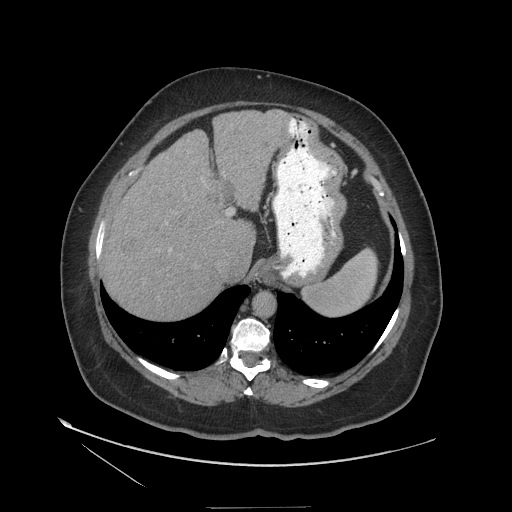
Contrast-enhanced abdominal CT (liver protocol), one axial slice; position 89 of 127 along the scan axis; reconstruction kernel STANDARD; 140 kVp; soft-tissue window (W 400 / L 40 HU); 2.5 mm slice thickness; 512 × 512 image matrix, field of view 480 × 480 mm. From the clinical record (not read from this slice): diagnosis: hepatocellular carcinoma (patient treated with transarterial chemoembolisation; whether this scan precedes or follows treatment is not stated here); TNM stage (as recorded): Stage-II; Child-Pugh class: A; tumour differentiation: well differentiated; tumour nodularity: multinodular.
Structures marked on this image (semi-automatic segmentation, software-assisted and operator-edited):
- abdominal aorta: box from (x=253, y=293) to (x=275, y=317) px
- liver parenchyma outside the tumour (the mass and vessels are separate outlines, so this box may not span the whole liver): (x=100, y=110)–(x=286, y=320)
- mass: (x=120, y=235)–(x=149, y=262)